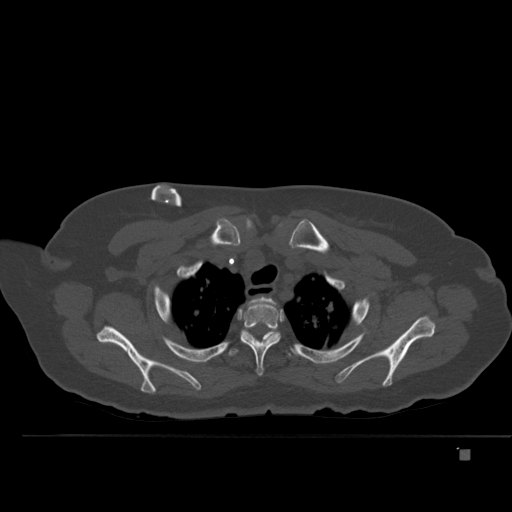
CT including the spine, one axial slice; slice 389 of 477 in the series (ordered by position); bone window (W 1800 / L 400 HU); 512 × 512 image matrix, field of view 422 × 422 mm. Female patient, age 74 years. From the clinical record (not read from this slice): primary cancer: colon.
Outlined on this slice (semi-automatic segmentation, software-assisted and operator-edited):
- T1 vertebra: bounding box (x1, y1, x2, y2) in pixels: (251, 297, 274, 304)
- T2 vertebra: (239, 303, 284, 375)
- T3 vertebra: (229, 330, 293, 357)